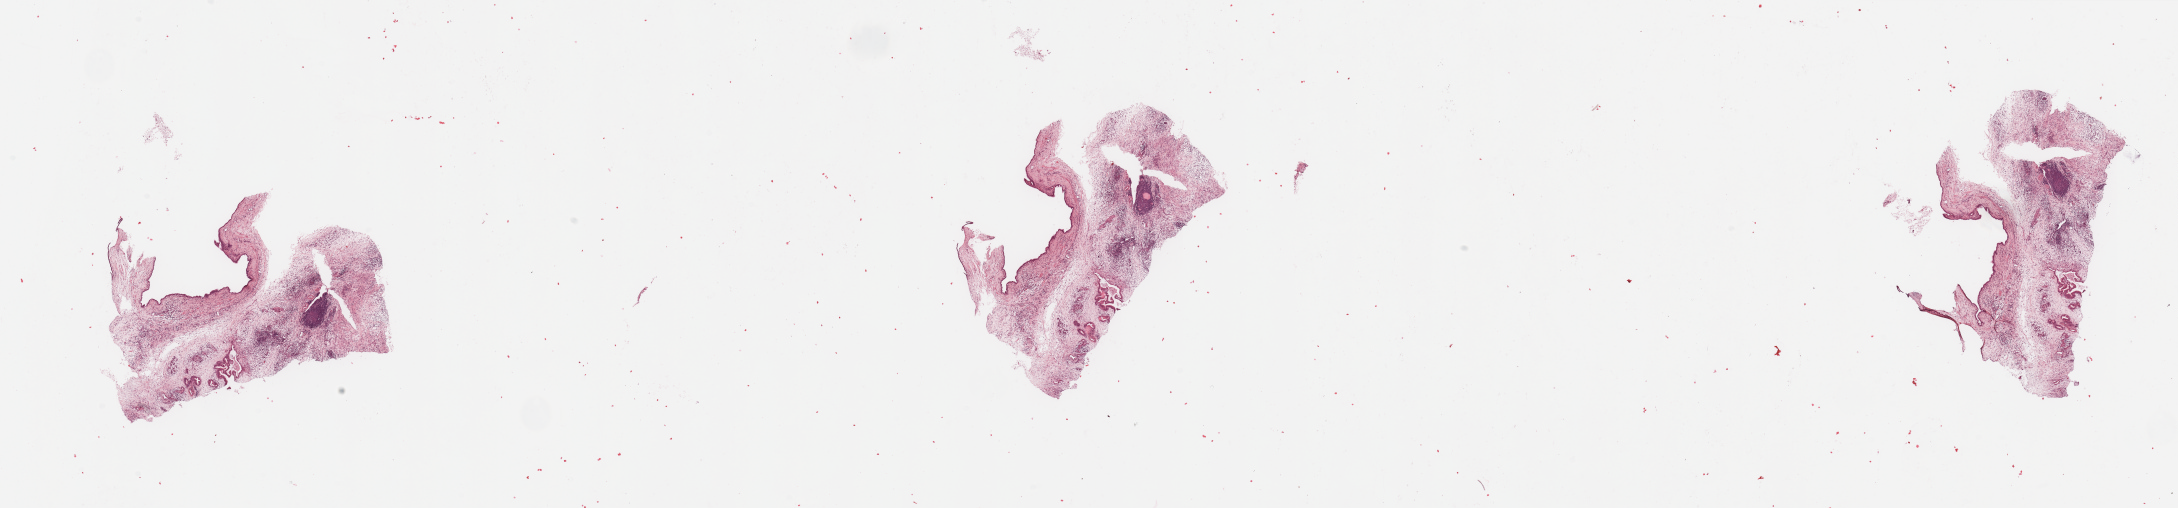
Digitized H&E tissue section (whole slide), low-resolution overview of the scanned area, about 34.5 x 8.0 mm (from a 20x scan). Tumour tissue sample, sampled site: pancreas. 56-year-old female patient. Histologic grade: G2 (moderately differentiated). Composition of this section per pathologist review: tumour nuclei 10%, necrosis 2%.
• diagnosis: Infiltrating duct carcinoma, NOS
• AJCC pathologic stage: IIB
• primary tumour site (as recorded): head